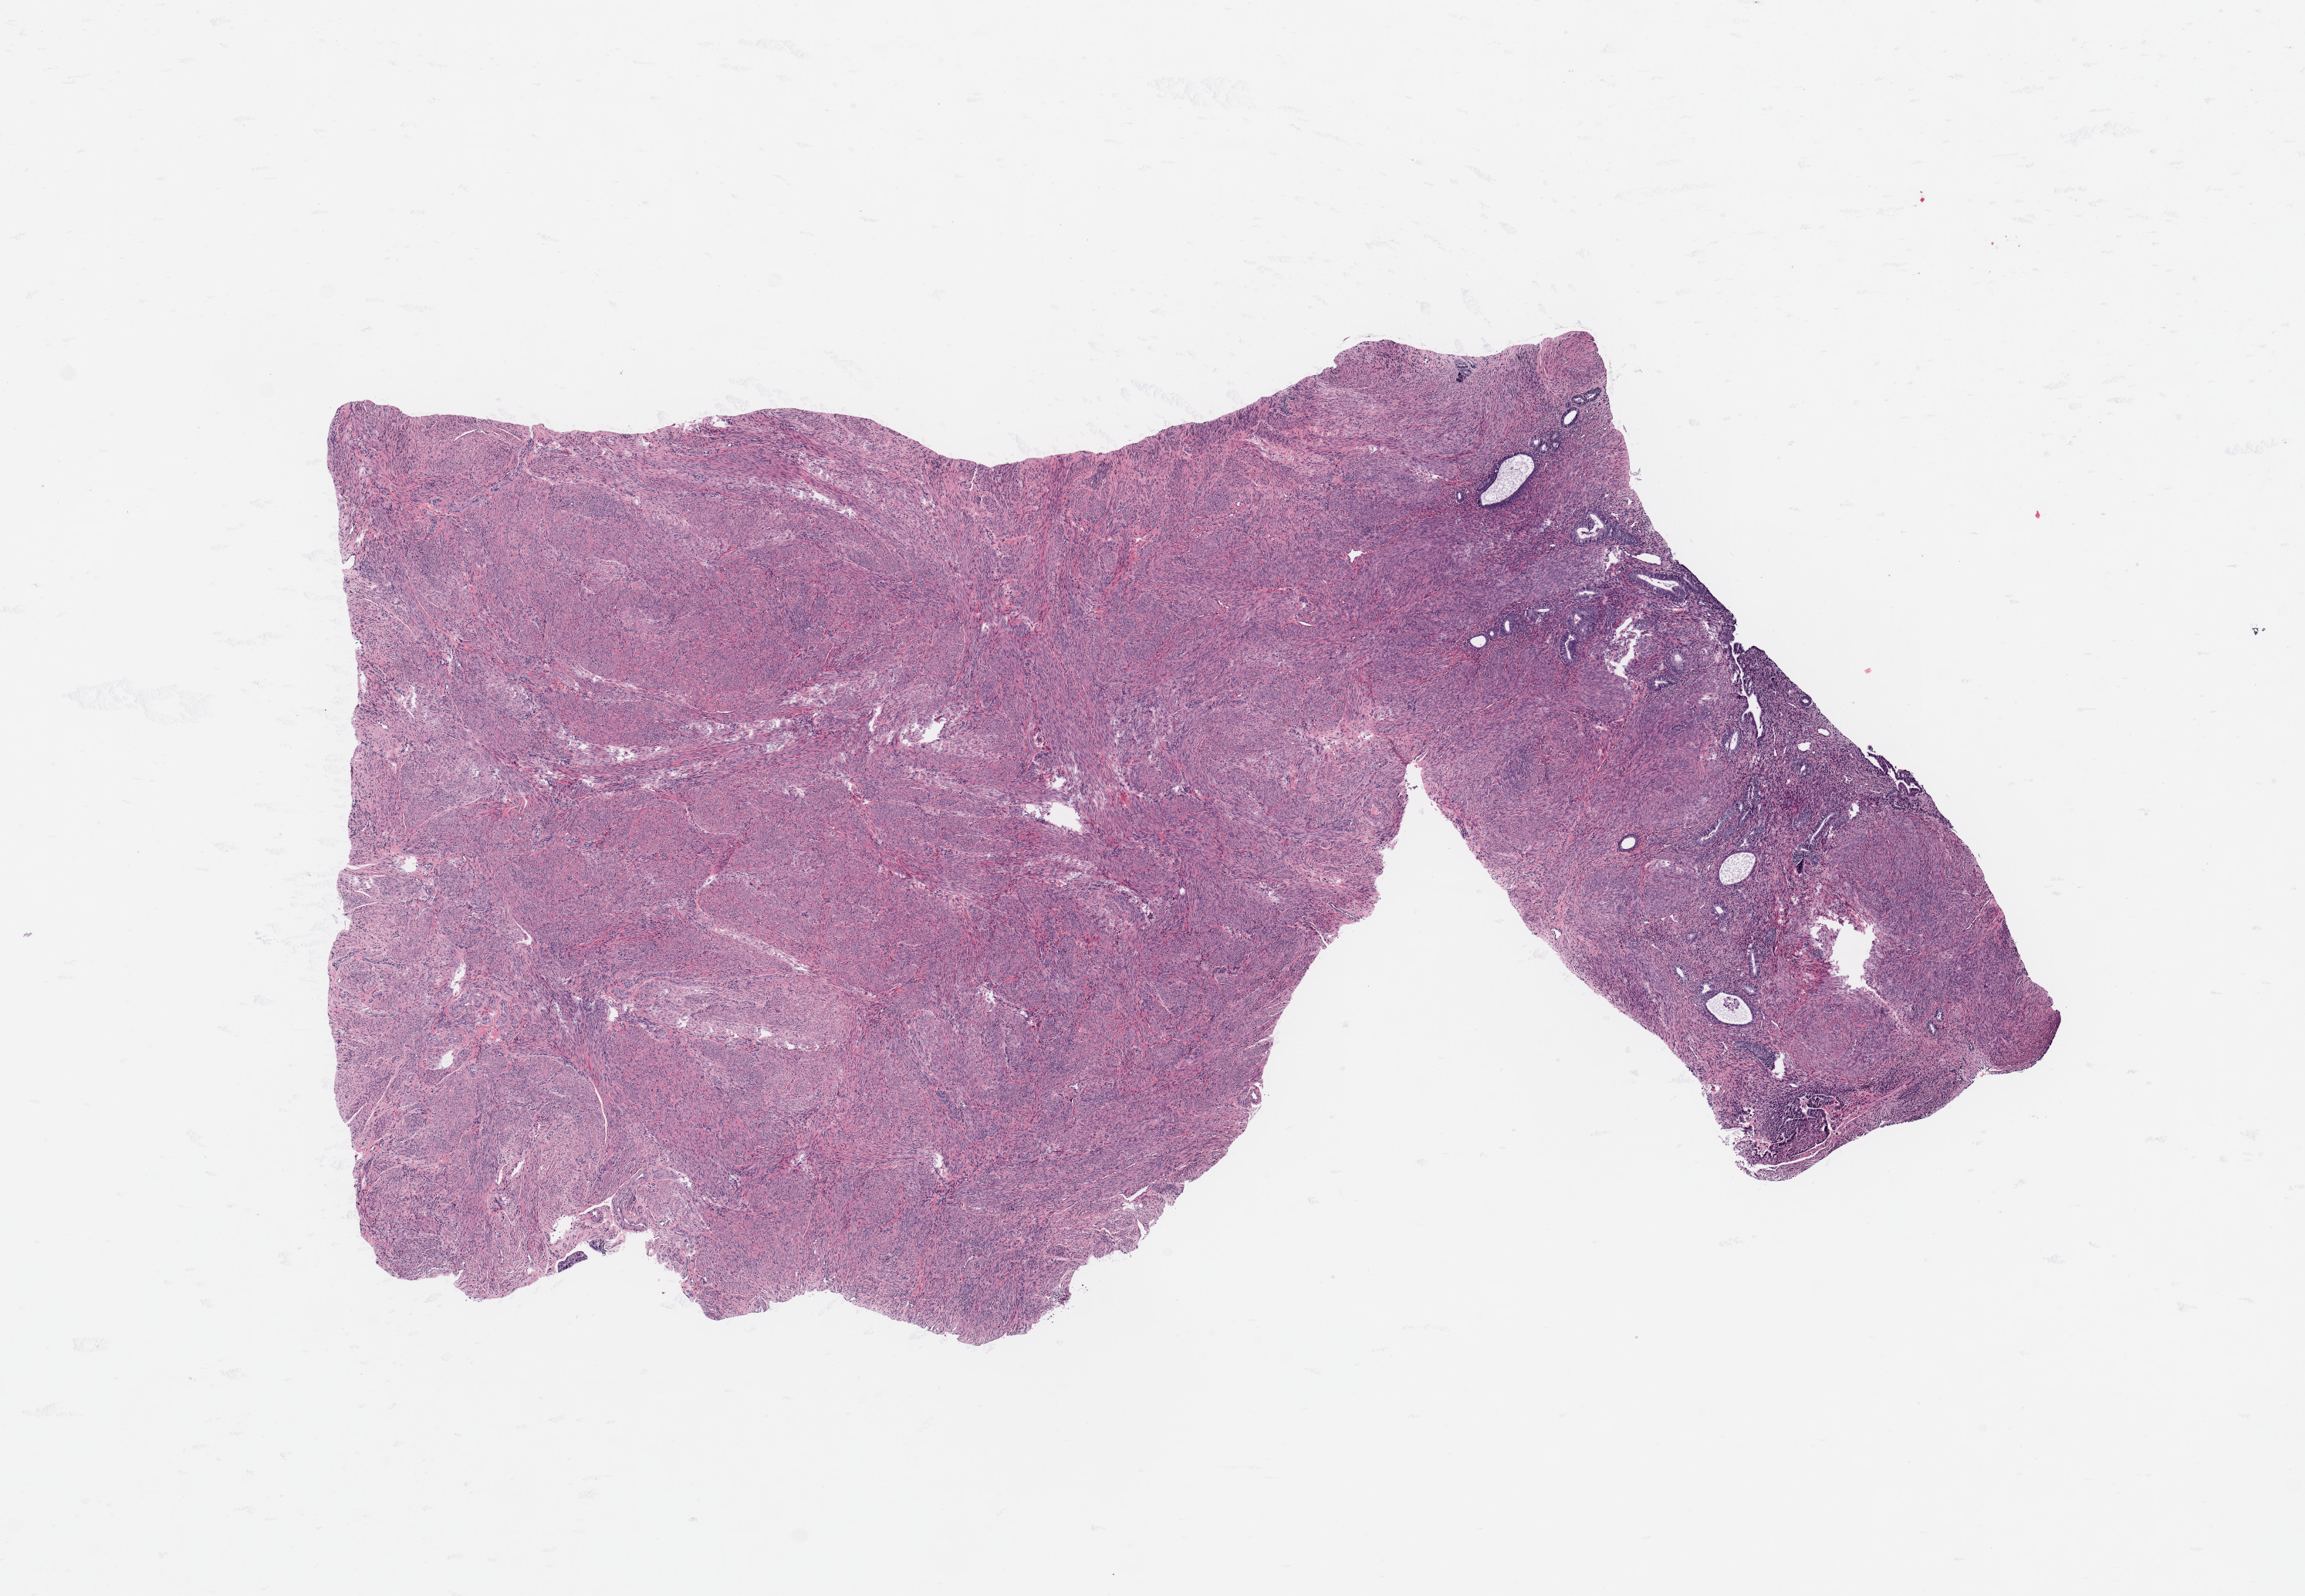
H&E whole-slide image — a low-resolution overview of the entire scanned area, about 11.8 x 8.2 mm; normal (non-tumour) tissue sample, uterus. 64-year-old female patient.
This section: normal (non-tumour) tissue from the same patient. Patient diagnosis: Endometrioid adenocarcinoma, NOS.